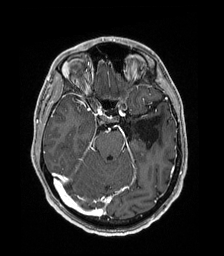
Brain MRI from a brain-tumour surgery series, one axial slice. Position 117 of 192 along the scan axis. T1-weighted post-contrast. 1 mm slice thickness. 224 × 256 image matrix, field of view 224 × 256 mm. From the clinical record (not read from this slice): histopathology: Low grade glioma; IDH mutation: no; tumour location: Left Parieto-Occipital Intraventricular.
Outlined on this slice (expert manual segmentation):
- previous resection cavity: bounding box (x1, y1, x2, y2) in pixels: (134, 117, 159, 149)